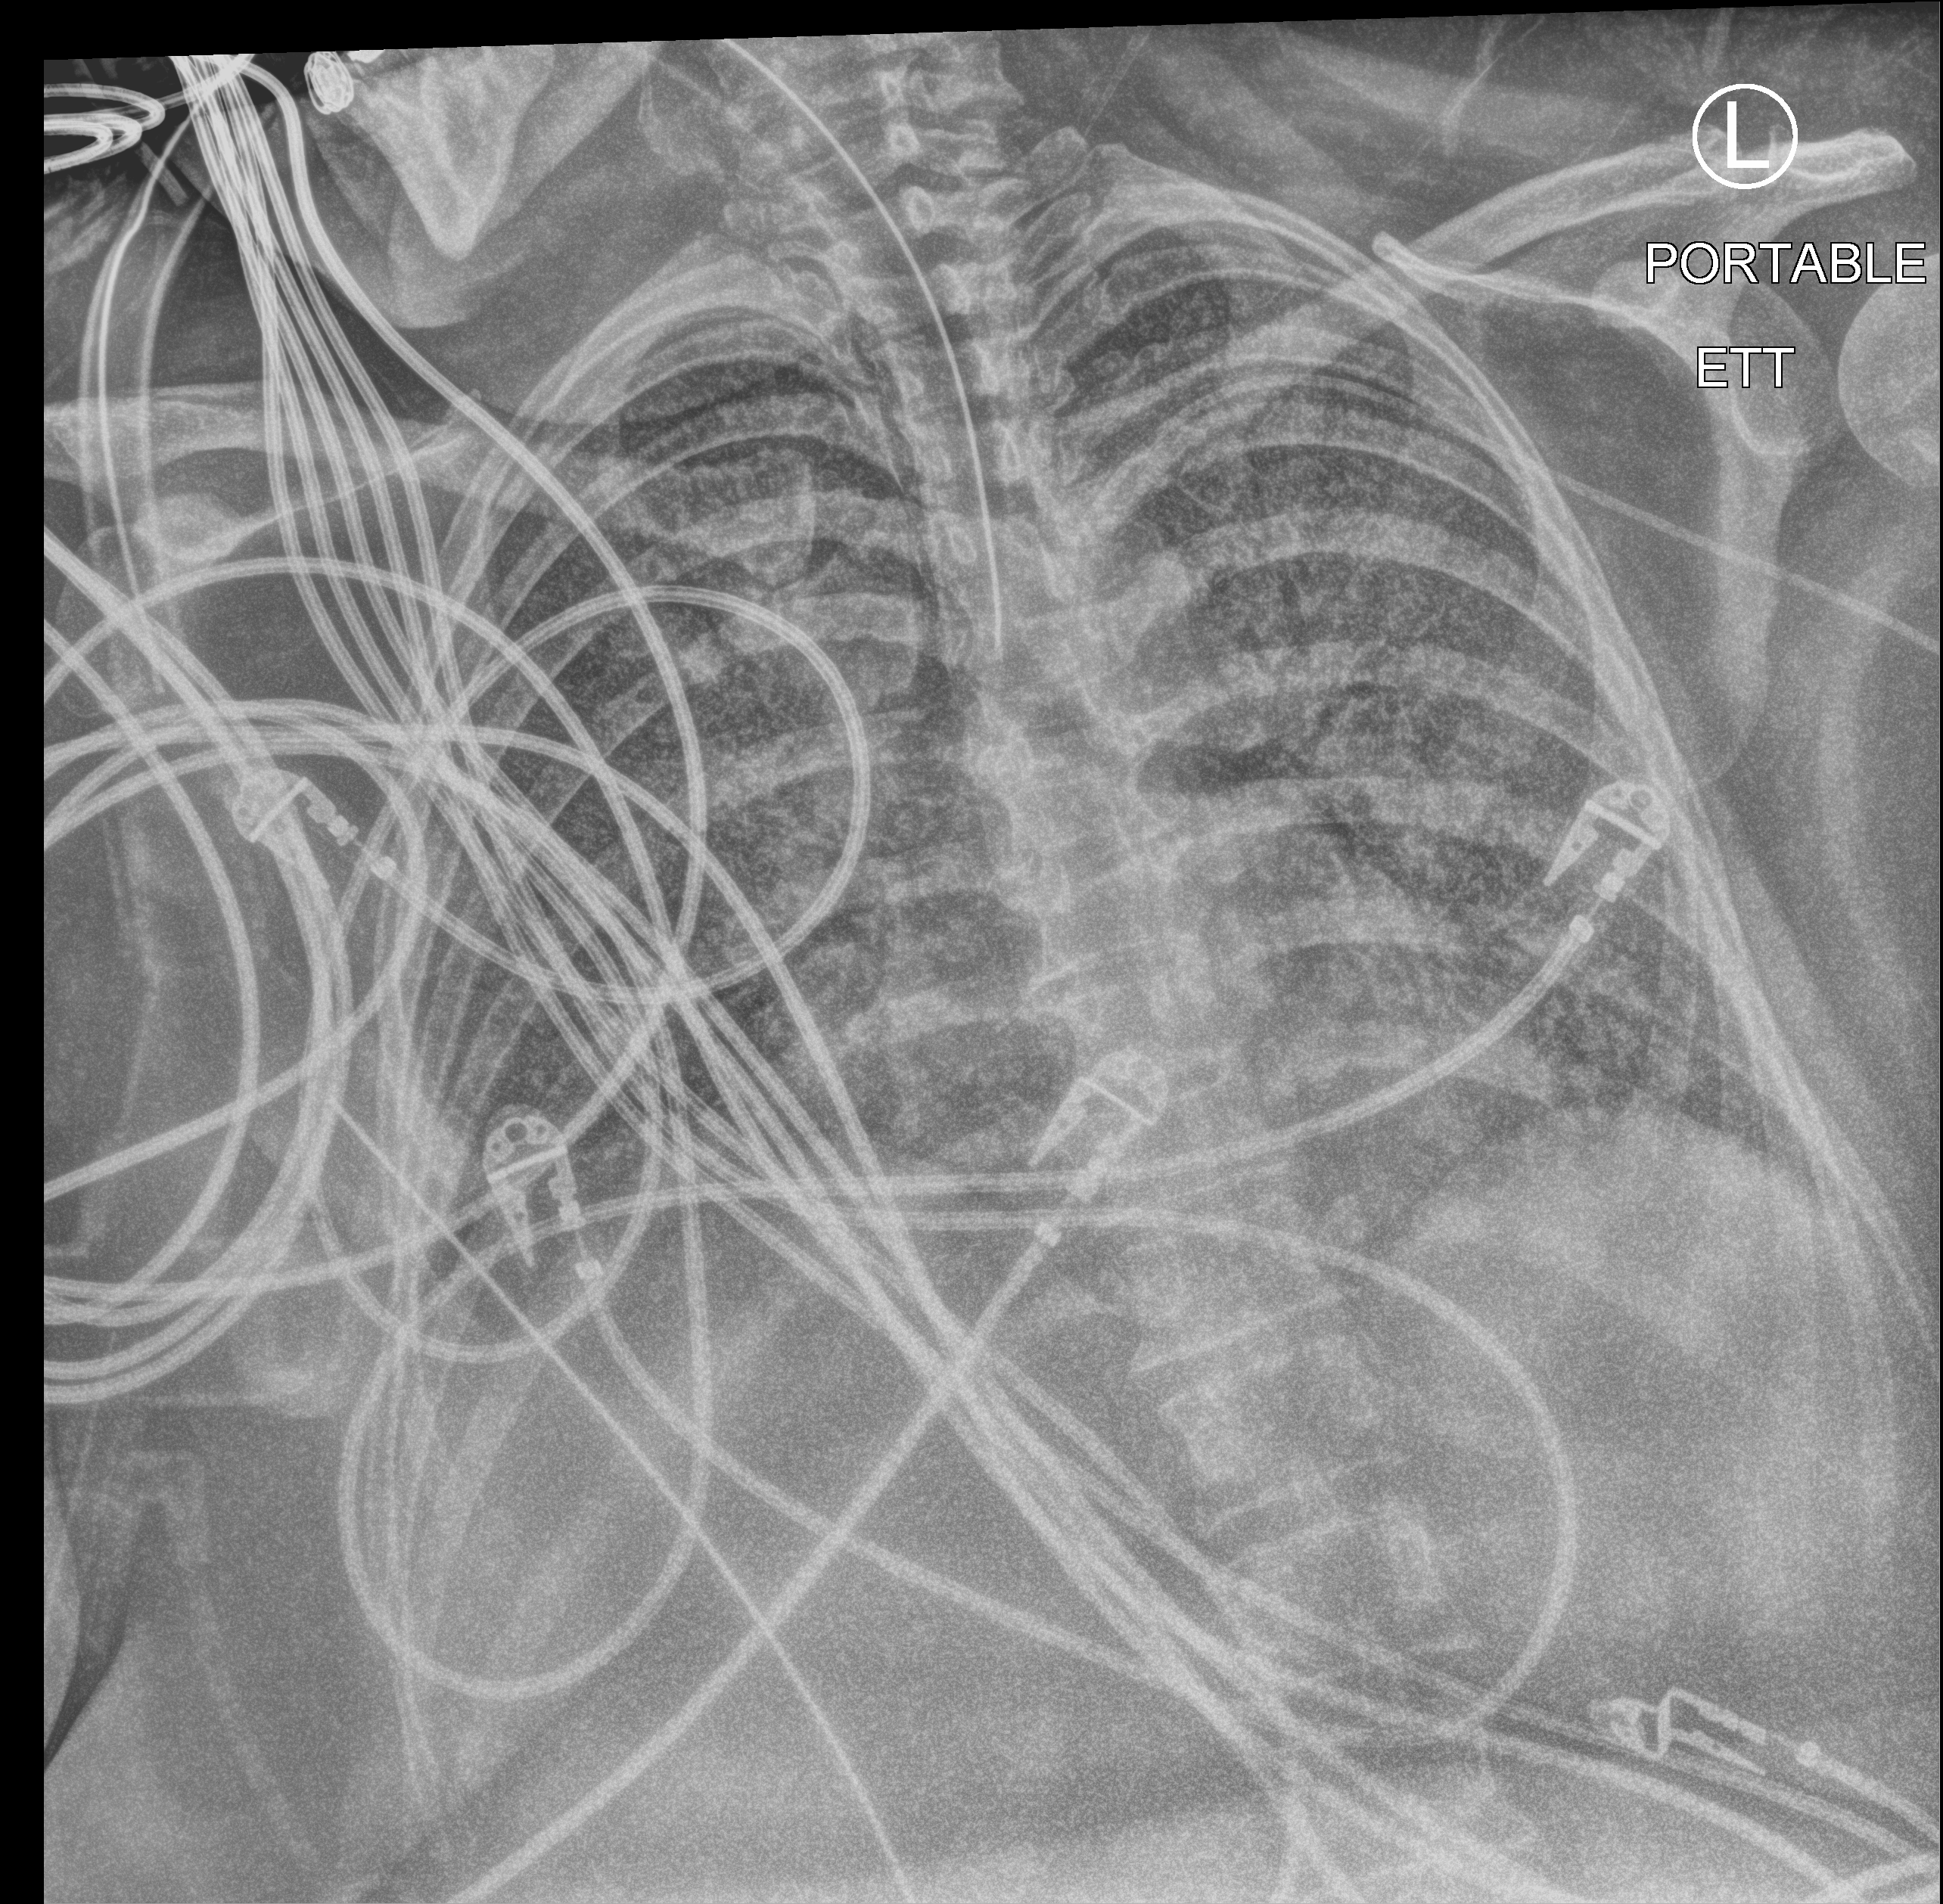
Bedside chest radiograph (computed radiography), anteroposterior (AP) projection. Patient hospitalised with COVID-19; female, aged 18–59 years.
Admission-level facts for this patient (not findings on this image; timing relative to this image not recorded): admitted to intensive care during this hospital stay: yes; length of hospital stay: 95 days; mechanically ventilated during this hospital stay: yes.